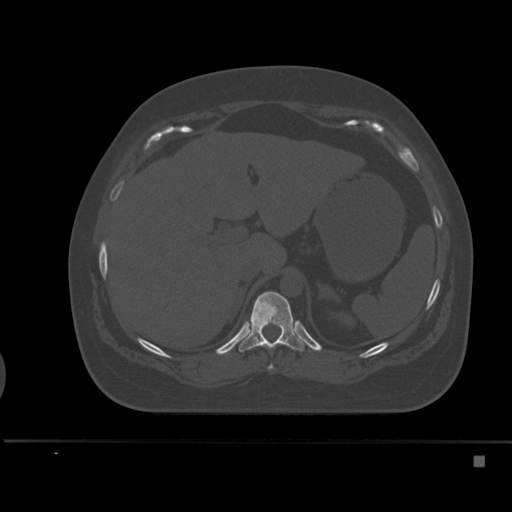
CT including the spine, one axial slice. Bone window (W 1800 / L 400 HU). 1.5 mm slice thickness. 512 × 512 image matrix, field of view 404 × 404 mm. Patient: female, 33 years. From the clinical record (not read from this slice): primary cancer: breast; vertebrae with lytic lesions (as recorded): T1.
Outlined on this slice (semi-automatically segmented with operator editing):
- T10 vertebra: bounding box (x1, y1, x2, y2) in pixels: (267, 364, 275, 370)
- T11 vertebra: (238, 291, 309, 352)